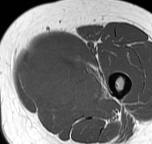
MRI of an extremity soft-tissue mass, one axial slice. Position 21 of 57 along the scan axis. MR volume resampled by the dataset authors to the PET/CT grid (not the native acquisition matrix). 152 × 144 image matrix. Female patient. Case-level facts recorded for this patient, not image findings: histological type: pleiomorphic leiomyosarcoma; grade: intermediate; site of the primary tumour: left thigh.
Annotated regions visible in this slice (expert contour drawn on MRI and transferred to this co-registered scan by the dataset authors):
- gross tumour volume including surrounding oedema: bounding box (x1, y1, x2, y2) in pixels: (18, 44, 108, 111)
- gross tumour volume (mass): (20, 46, 101, 111)